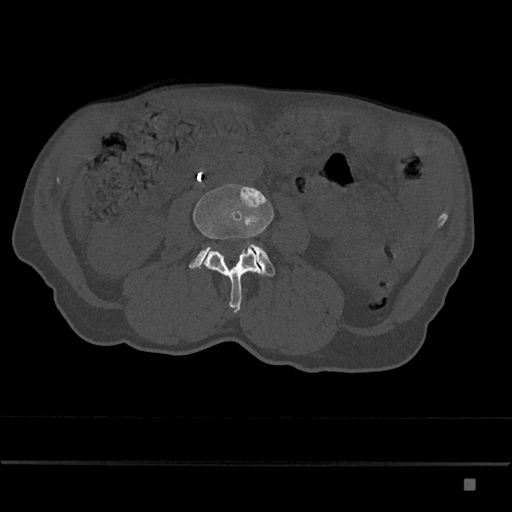
CT including the spine, one axial slice. Slice 384 of 797 in the series (ordered by position). Reconstruction kernel Br40s/3. 120 kVp. Bone window (W 1800 / L 400 HU). 512 × 512 image matrix, field of view 390 × 390 mm. Patient: male, 72 years. Case-level facts recorded for this patient, not image findings: primary cancer: prostate.
Structures marked on this image (semi-automatic segmentation, software-assisted and operator-edited):
- L3 vertebra: bounding box (x1, y1, x2, y2) in pixels: (193, 184, 274, 313)
- L4 vertebra: (189, 244, 275, 277)